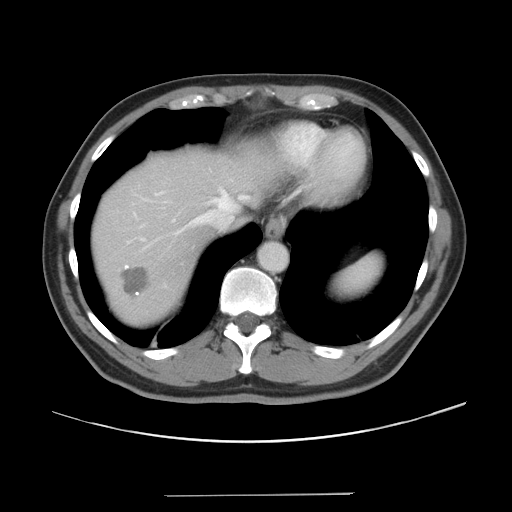
Contrast-enhanced abdominal CT, one axial slice. Slice 35 of 43 in the series (ordered by position). Reconstruction kernel STANDARD. 120 kVp. Intravenous contrast given. Soft-tissue window (W 400 / L 40 HU). 5 mm slice thickness. 512 × 512 image matrix. Male patient, age 65 years. From the clinical record (not read from this slice): diagnosis: colorectal cancer liver metastases, imaged before liver resection; multiple liver metastases: no; largest metastasis: 3.8 cm.
Structures marked on this image (expert manual segmentation):
- hepatic veins: bounding box <176,188,248,234> (left, top, right, bottom; pixels)
- liver: <95,153,271,324>
- planned liver remnant (the part of the liver to remain after resection): <95,153,271,285>
- liver metastasis: <122,266,149,298>